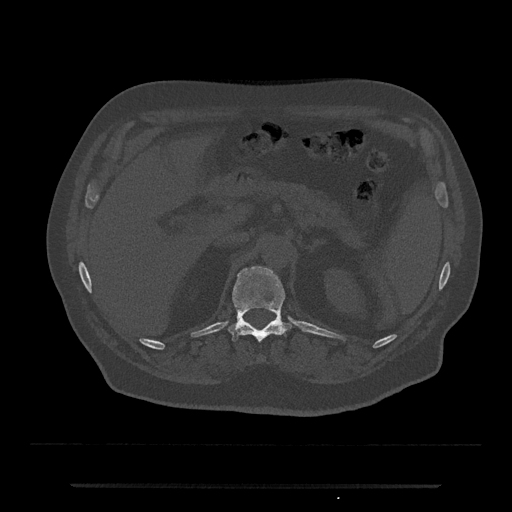
CT including the spine, one axial slice. Slice 592 of 797 in the series (ordered by position). Bone window (W 1800 / L 400 HU). 0.5 mm slice thickness. 512 × 512 image matrix, field of view 434 × 434 mm. Male patient, age 80 years. Case-level facts recorded for this patient, not image findings: primary cancer: prostate.
Outlined on this slice (semi-automatic segmentation, software-assisted and operator-edited):
- T12 vertebra: box from (x=228, y=266) to (x=291, y=342) px